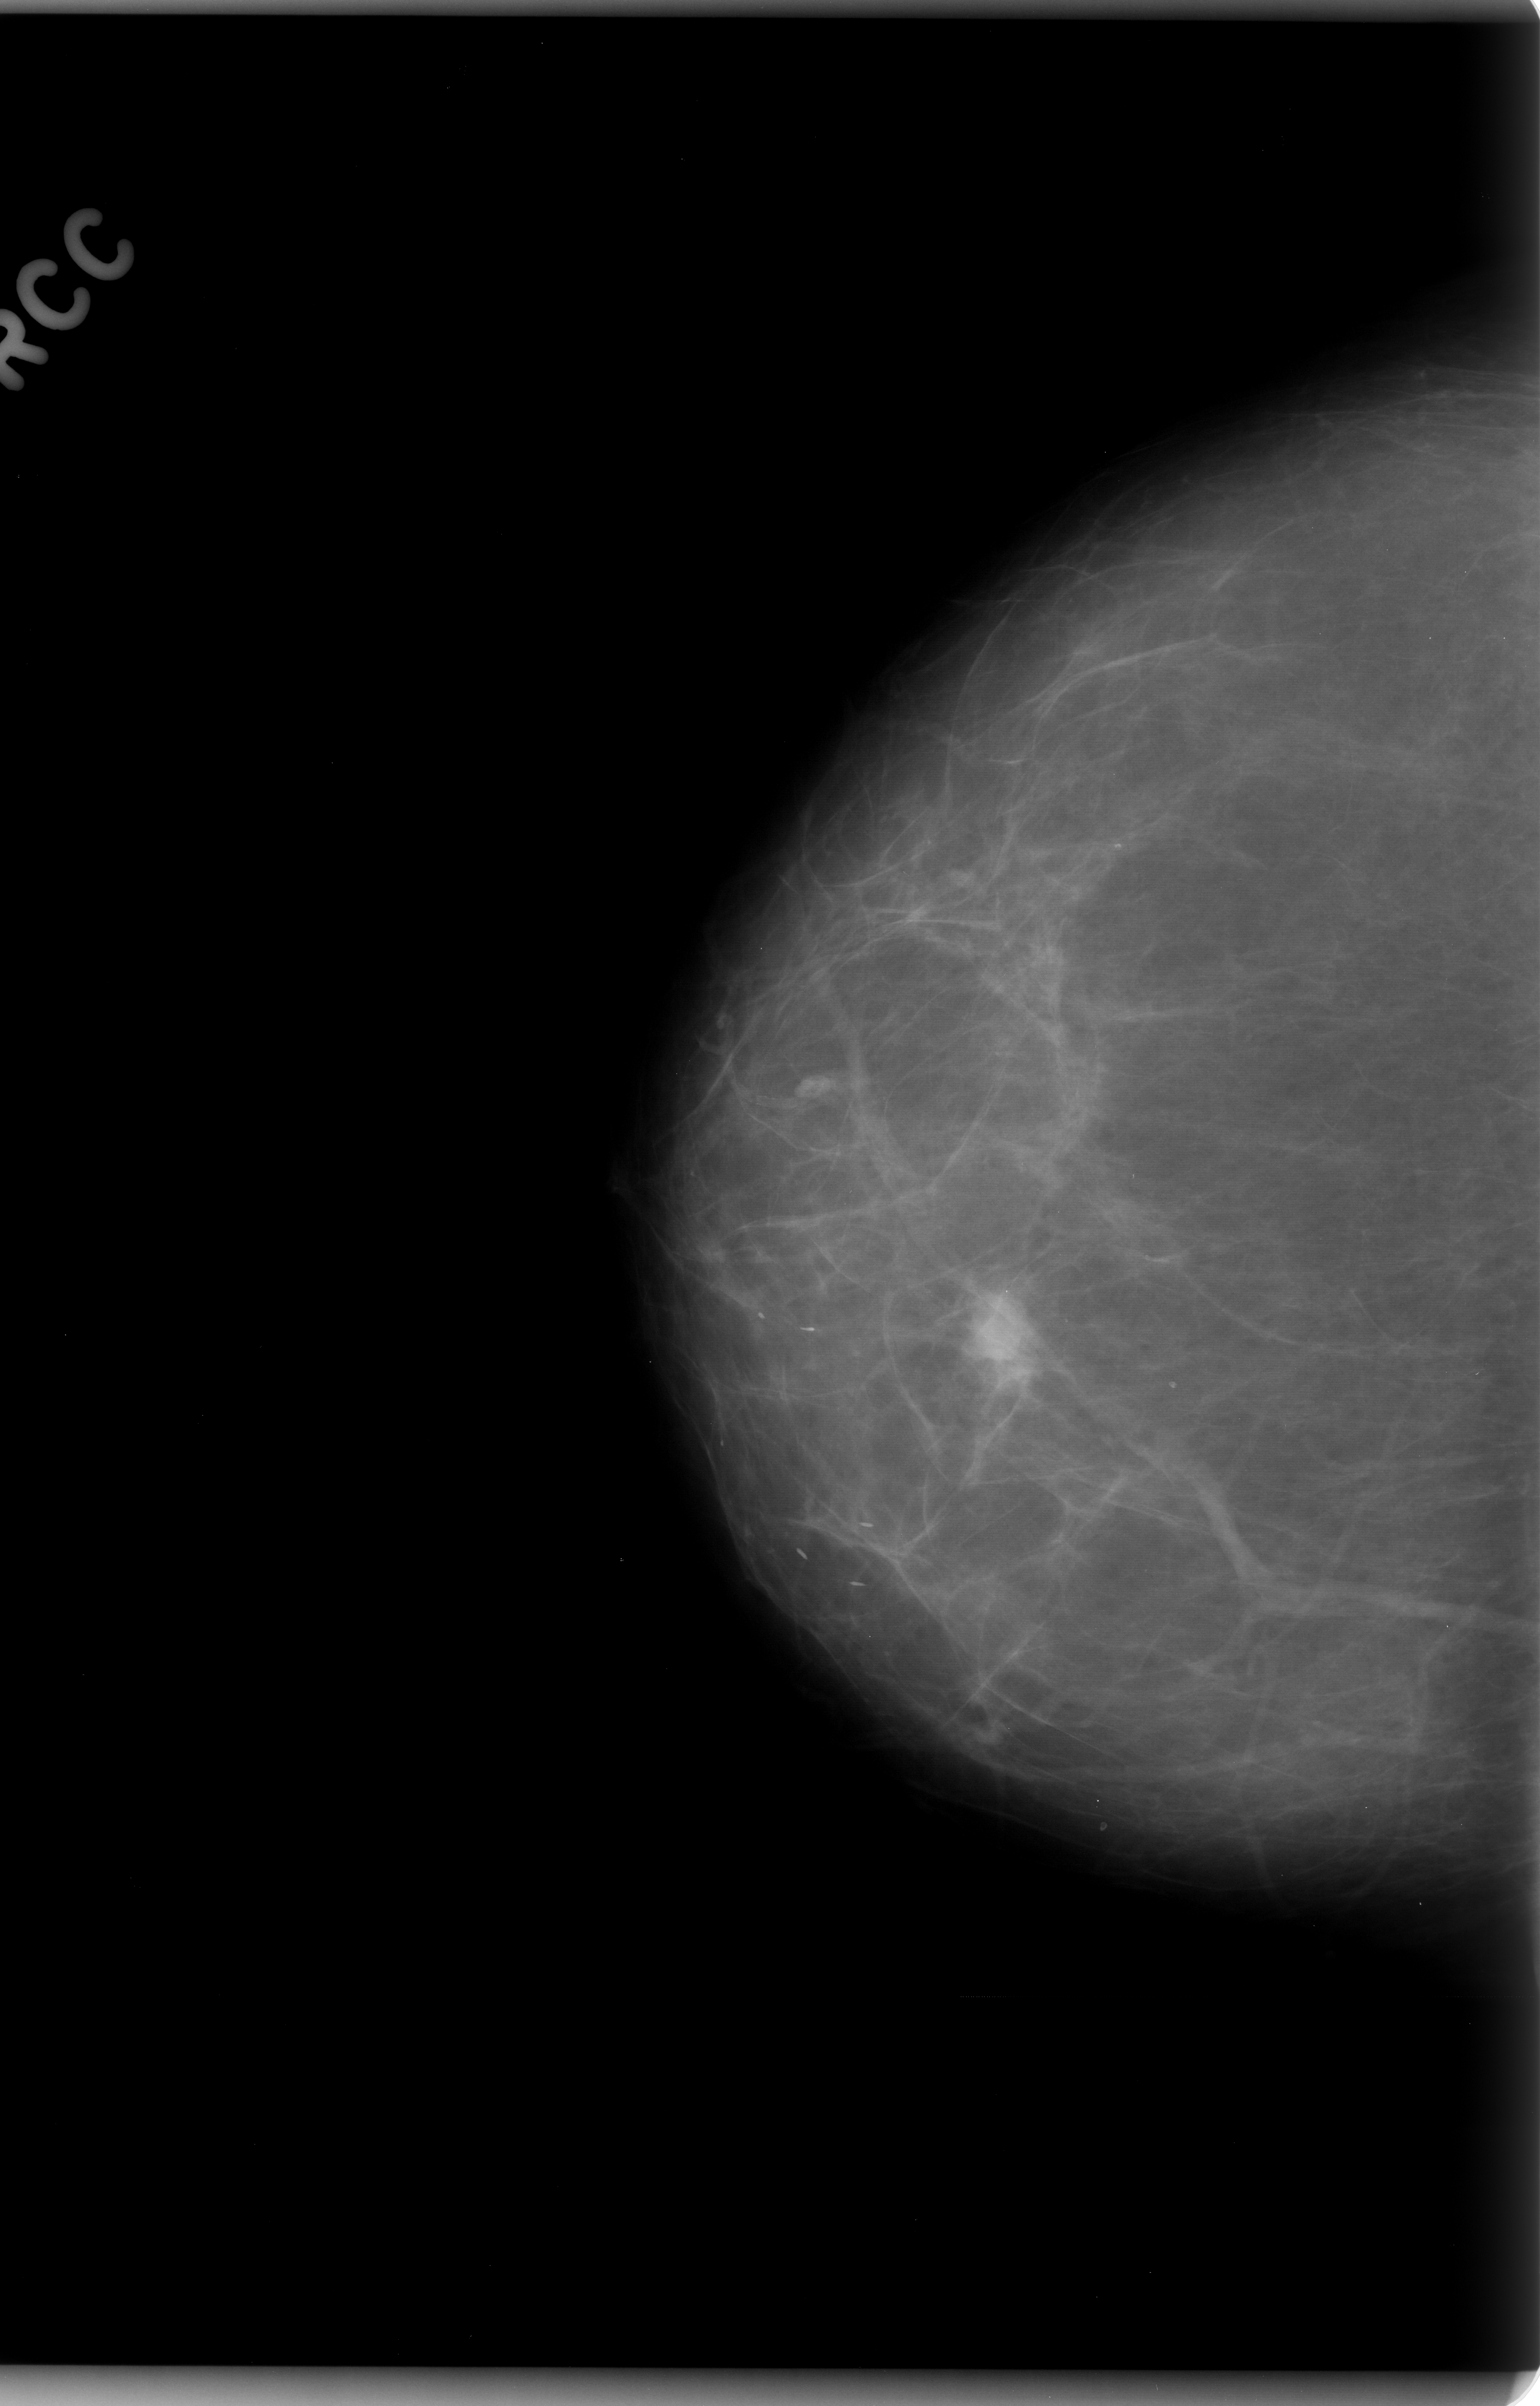
Digitized screen-film mammogram. Right breast. Craniocaudal (CC) view. Breast composition: almost entirely fatty (BI-RADS density category 1 of 4). 1540 × 2406 image matrix.
Marked abnormalities (boxes around the expert regions of interest):
- mass, shape lobulated, margins microlobulated; BI-RADS assessment category 5; subtlety rating 5 on a 1 (subtle) to 5 (obvious) scale; pathology result (as recorded, not read from the image): malignant: bounding box <954,1274,1068,1408> (left, top, right, bottom; pixels)